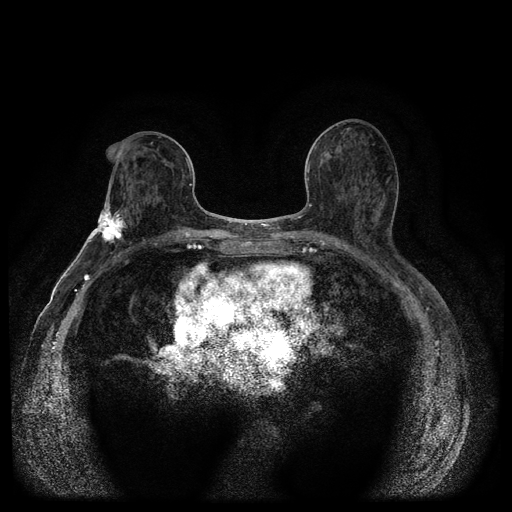
Breast MRI (dynamic contrast-enhanced, multi-phase), one axial slice; slice 52 of 116 in the series (ordered by position); dynamic contrast-enhanced series, time point 2 of 5 at this slice position (early post-contrast); 1.5 T; TE 2.7 ms, TR 5.4 ms; 512 × 512 image matrix, field of view 340 × 340 mm. Patient: female, 75 years.
Annotated regions visible in this slice (semi-automatic segmentation, software-assisted and operator-edited):
- breast lesion (labelled 'tumour' in the annotation; benign lesions carry a separate 'benign' label): bounding box <88,203,129,248> (left, top, right, bottom; pixels)